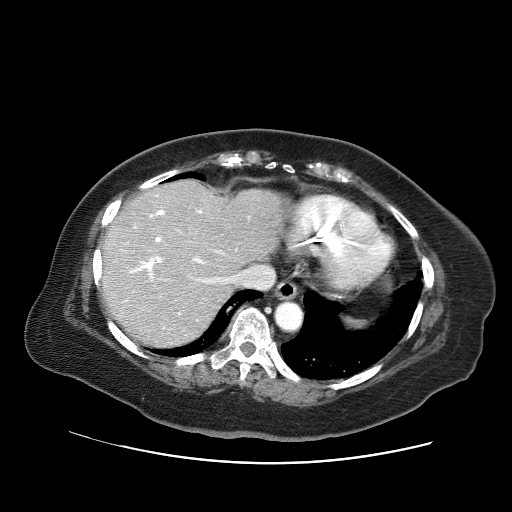
Contrast-enhanced abdominal CT (liver protocol), one axial slice; position 51 of 71 along the scan axis; 120 kVp; soft-tissue window (W 400 / L 40 HU); 512 × 512 image matrix, field of view 400 × 400 mm. Case-level facts recorded for this patient, not image findings: diagnosis: hepatocellular carcinoma (patient treated with transarterial chemoembolisation; whether this scan precedes or follows treatment is not stated here); TNM stage (as recorded): Stage-II; Child-Pugh class: A; tumour differentiation: poorly differentiated.
Structures marked on this image (semi-automatically segmented with operator editing):
- liver parenchyma outside the tumour (the mass and vessels are separate outlines, so this box may not span the whole liver): bounding box [x1, y1, x2, y2] px = [100, 180, 284, 346]
- liver vessels: [124, 195, 237, 329]